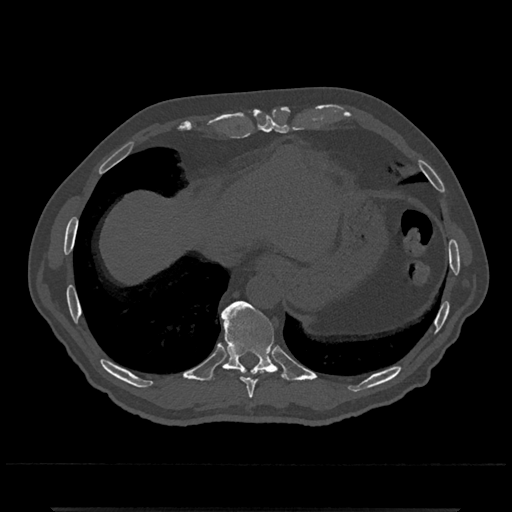
CT including the spine, one axial slice; position 578 of 797 along the scan axis; bone window (W 1800 / L 400 HU); 0.5 mm slice thickness; 512 × 512 image matrix, field of view 393 × 393 mm. Male patient, age 67 years. From the clinical record (not read from this slice): primary cancer: prostate.
Outlined on this slice (semi-automatic segmentation, software-assisted and operator-edited):
- T10 vertebra: bounding box <221,301,288,383> (left, top, right, bottom; pixels)
- T9 vertebra: <241,378,256,399>